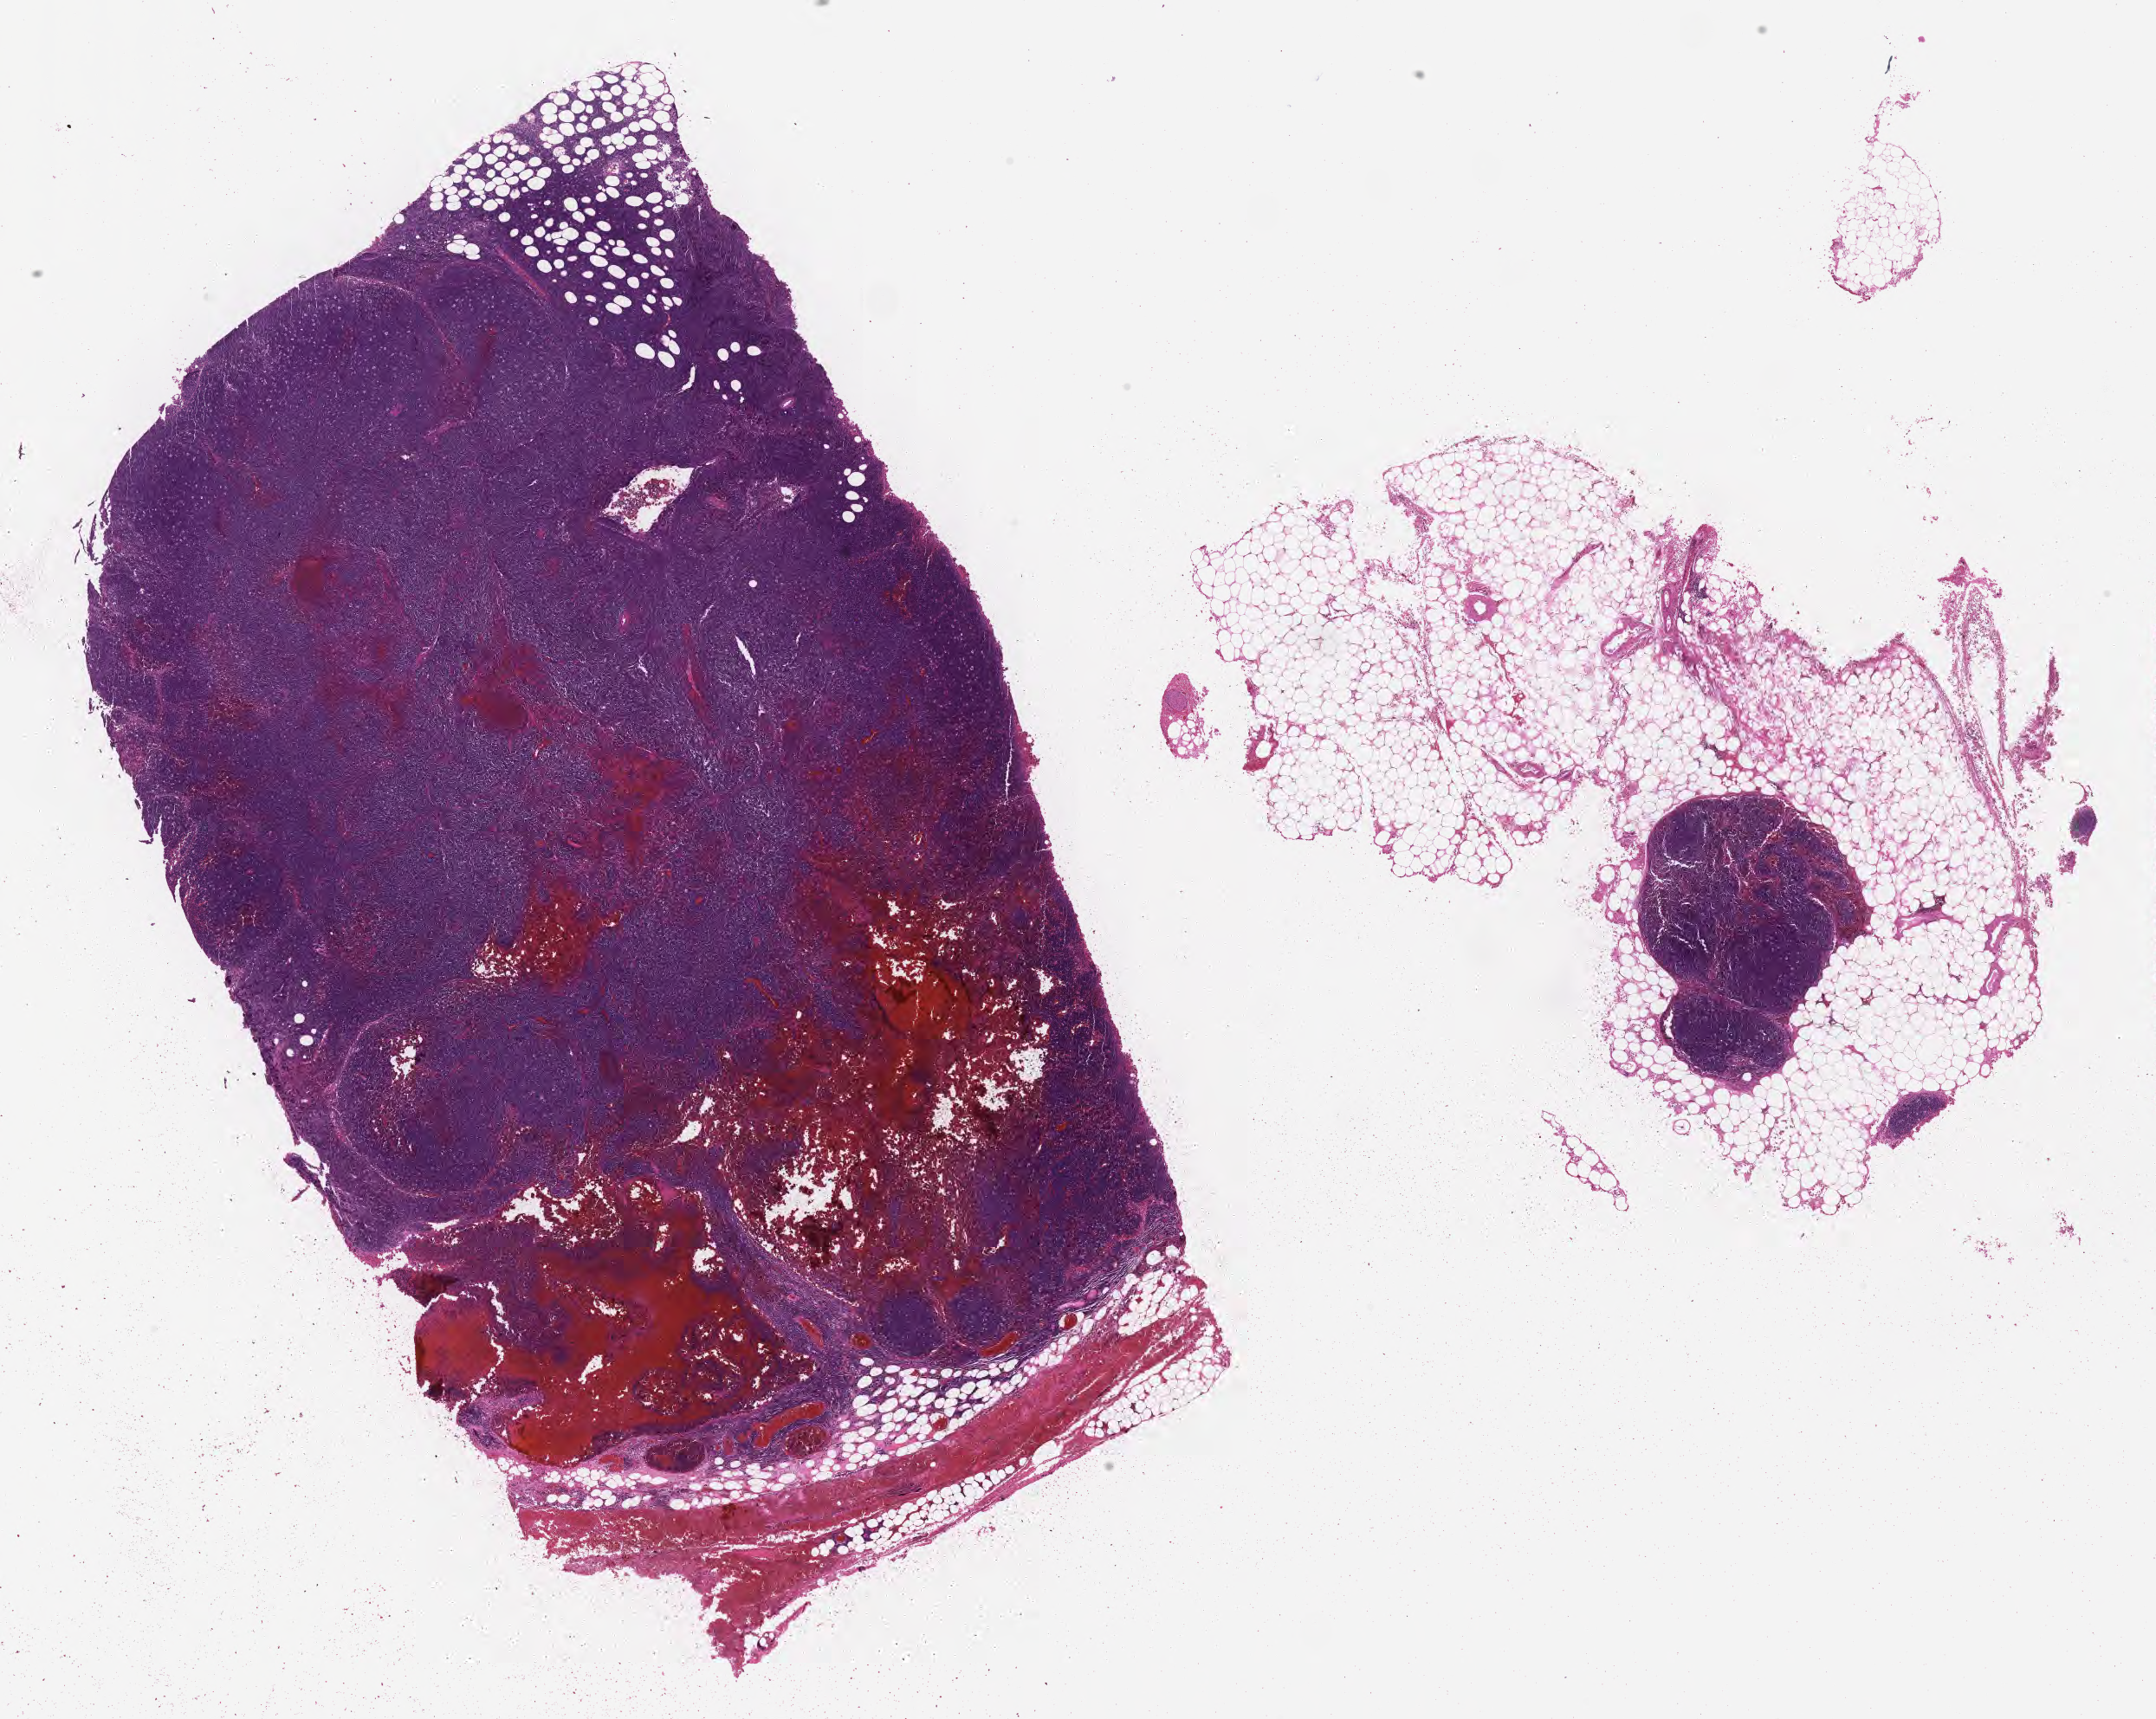
Whole-slide image, H&E stain, a low-resolution overview of the entire scanned area, about 20.1 x 16.1 mm, formalin-fixed, paraffin-embedded (FFPE) tissue, primary tumor. Male patient, age 40 years. Composition of this section per pathologist review: tumor cells 90%, tumor nuclei 95%, stromal cells 10%, necrosis 0%, normal cells 0%. Inflammatory infiltration, as recorded: lymphocyte infiltration 40%, monocyte infiltration 25%, neutrophil infiltration 5%.
* Ann Arbor stage (patient): Stage IV
* diagnosis: Burkitt lymphoma, NOS
* section: top of the tissue portion